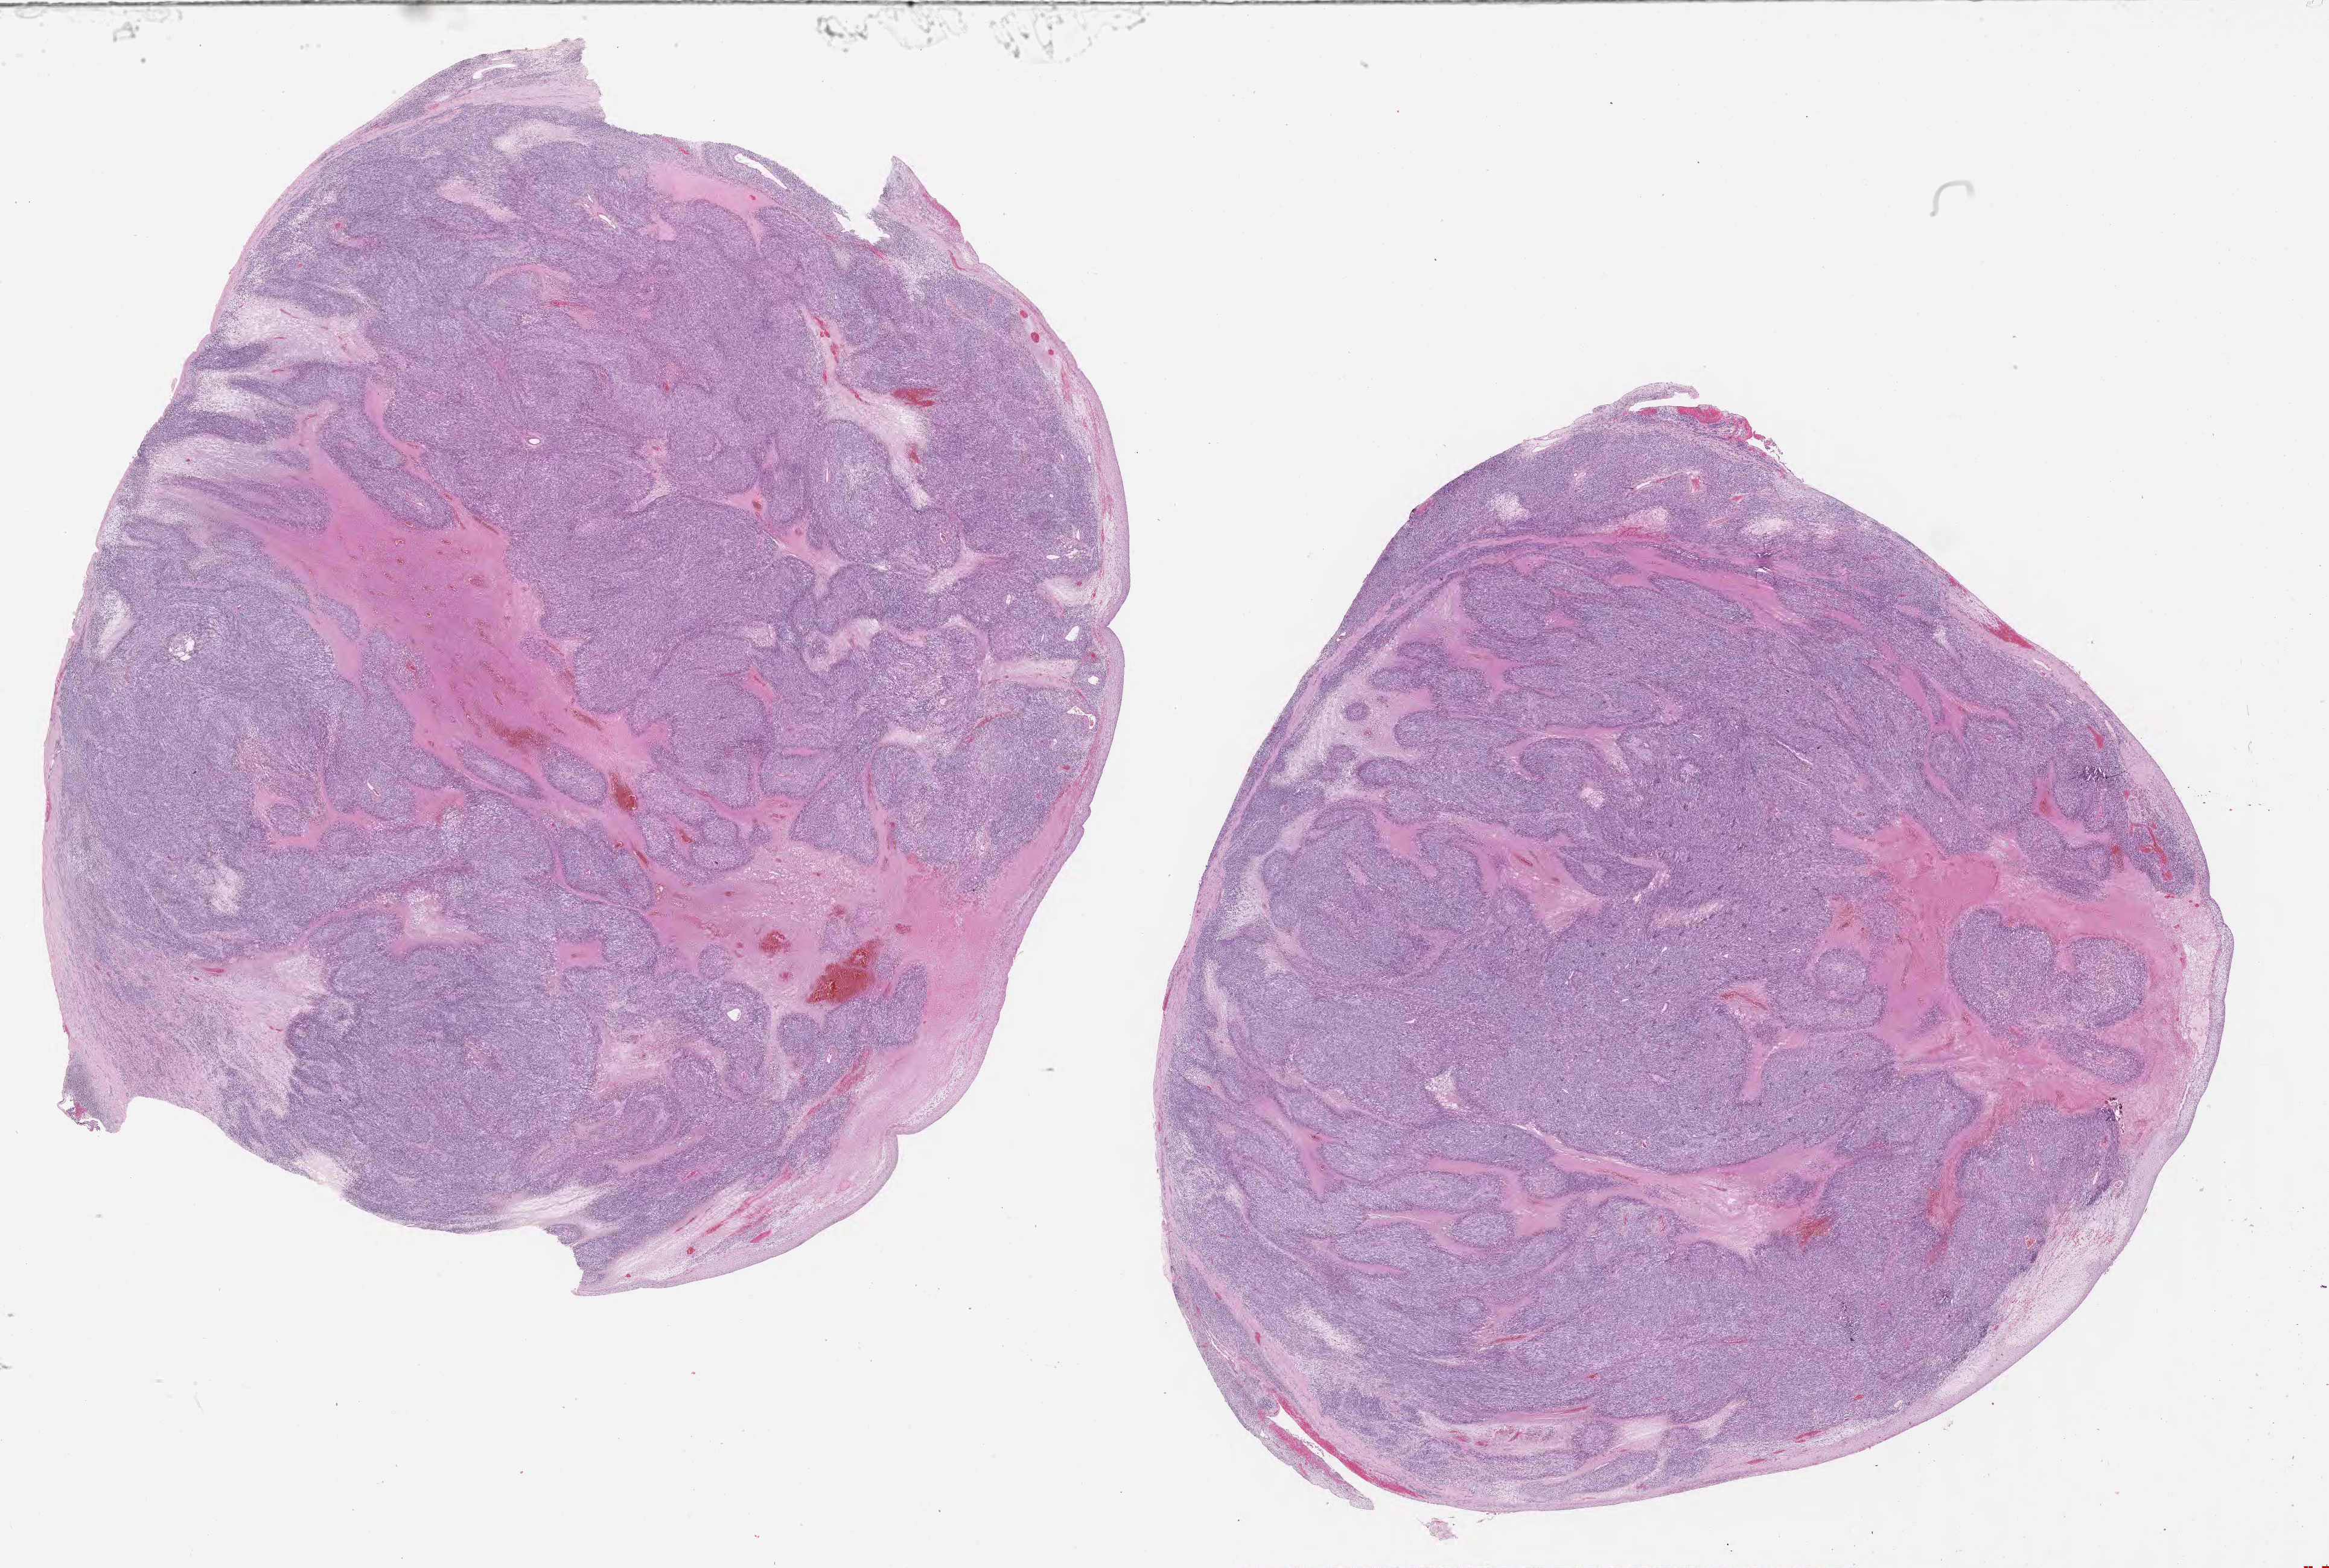
Digitized haematoxylin and eosin-stained section of tumor tissue, a low-resolution overview of the entire scanned area, about 31.2 x 21.0 mm; formalin-fixed, paraffin-embedded (FFPE) tissue; site: soft tissue - testicle, right. Male patient, age at diagnosis 8.2 years.
• metastatic status at presentation (as recorded): non-metastatic
• stage (as recorded): 1
• diagnosis: rhabdomyosarcoma; histological classification: embryonal rhabdomyosarcoma